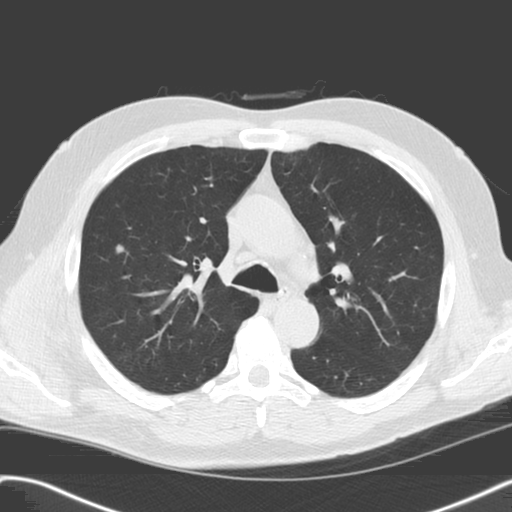
Low-dose screening chest CT, axial slice, baseline screening round, lung window (W 1500 / L -600 HU), slice 55 of 157 in the series, 512 × 512 image matrix, field of view 360 × 360 mm. Male, age 61 years at enrolment.
Expert reader's lesion annotation, bounding box [x1, y1, x2, y2] px = [105, 233, 136, 267]. Reader record for this screening exam (exam-level; its link to the box is not recorded): non-calcified nodule or mass ≥4 mm, right upper lobe, 6 × 6 mm, smooth margins, soft tissue attenuation. Official screen result: positive, change unspecified: nodule(s) >= 4 mm or enlarging nodule(s), mass(es), or other non-specific abnormalities suspicious for lung cancer. Participant outcome: lung cancer diagnosed 746 days after this screen — adenocarcinoma, NOS, right upper lobe, stage IIIA (AJCC 6th edition), 13 mm at pathology.